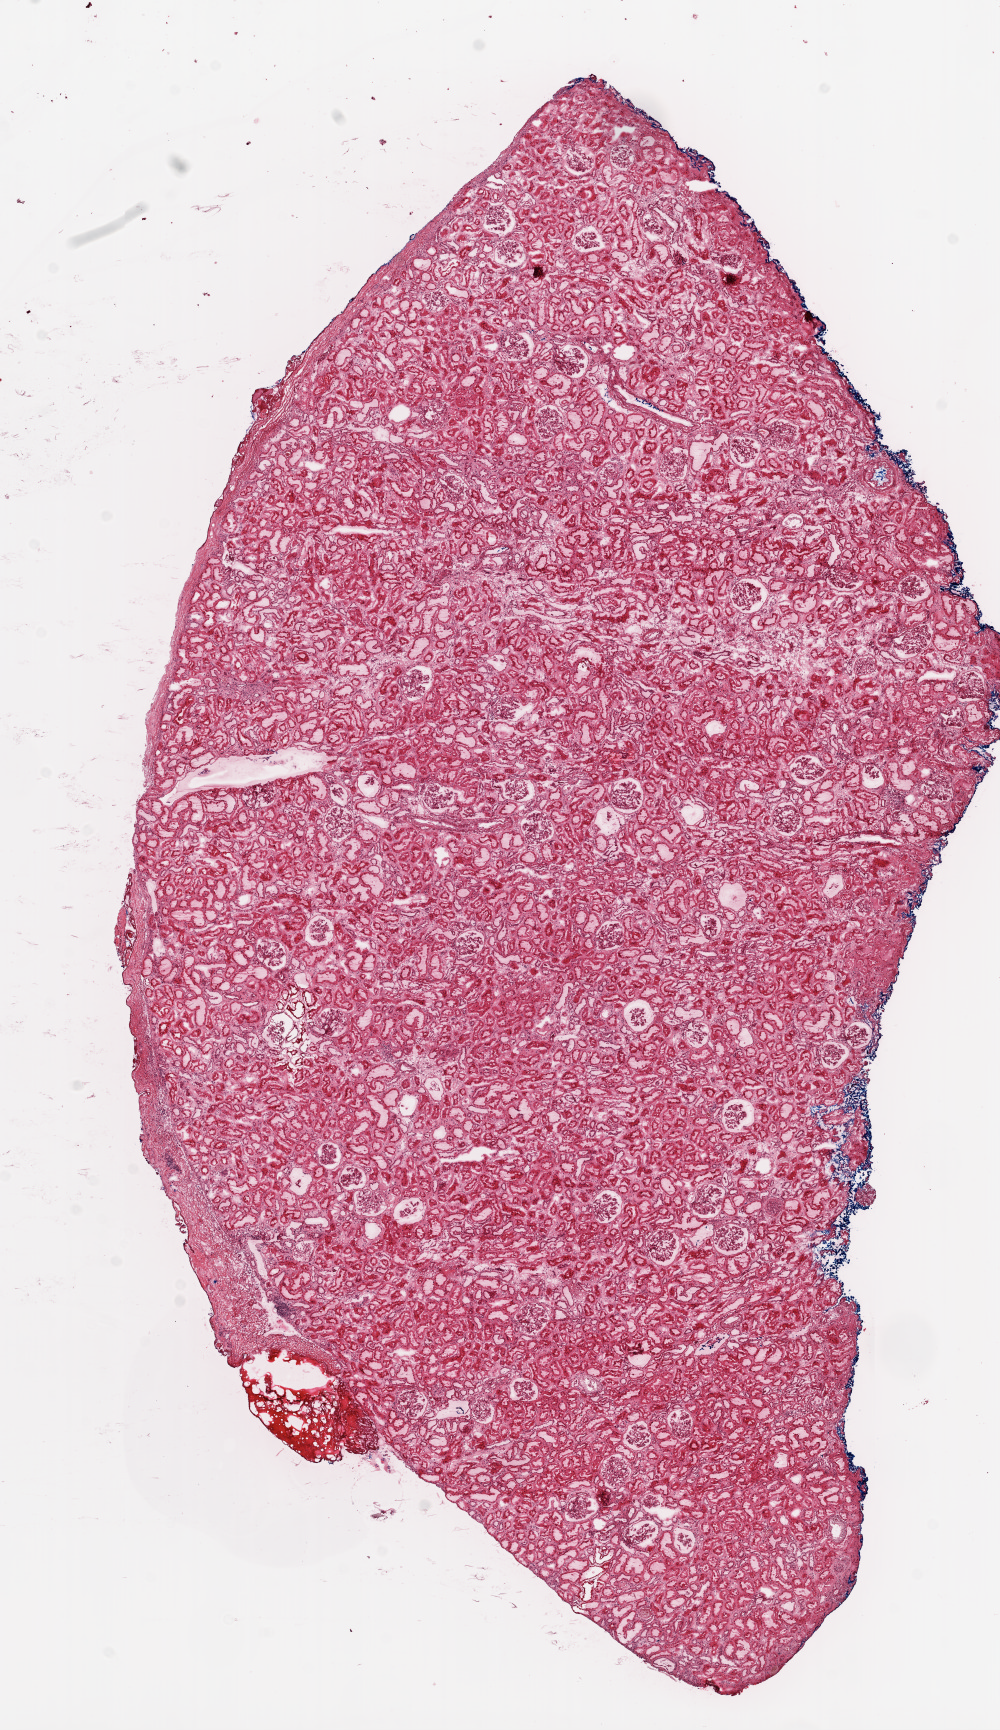
H&E whole-slide image — low-resolution overview of the scanned area, about 8.0 x 13.9 mm (acquisition: 20x scan); frozen section from the top of the tissue portion; kidney, solid tissue normal (non-tumour tissue) sample. Patient: female, age at initial diagnosis 55 years.
* this section: solid tissue normal (non-tumour) sample from the same patient
* patient diagnosis: Clear cell adenocarcinoma, NOS